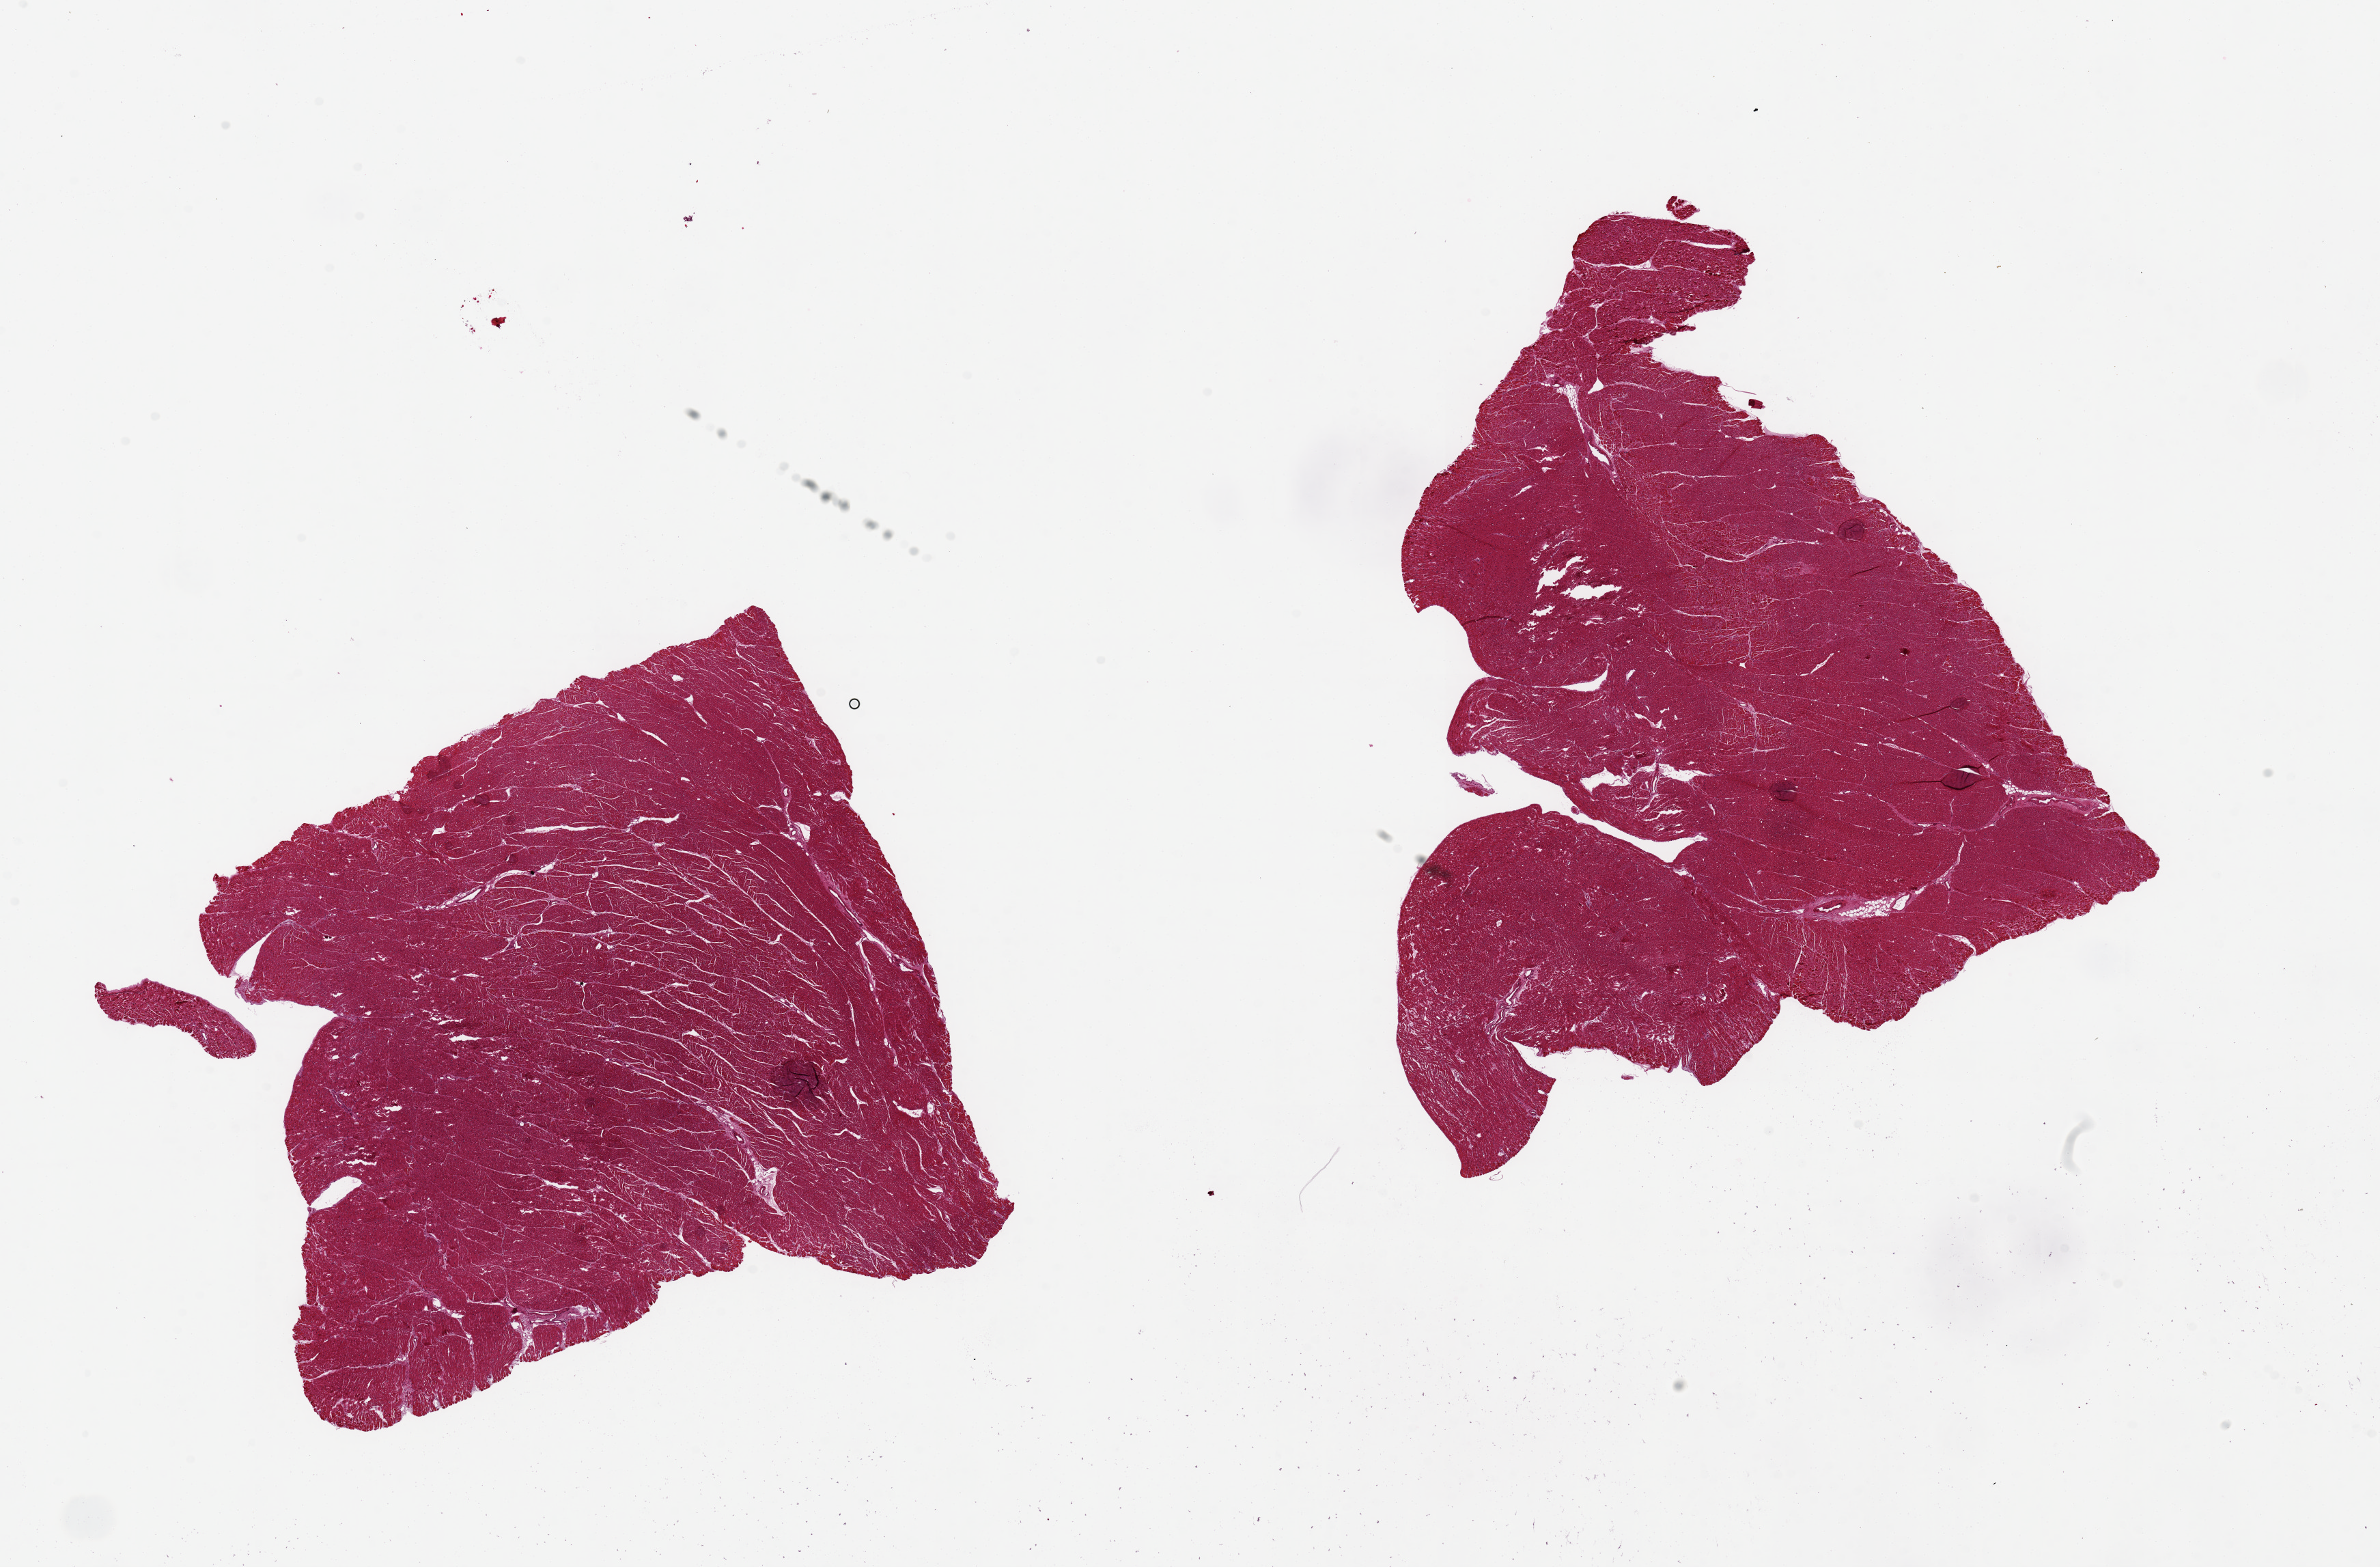
Whole-slide image, hematoxylin and eosin (H&E) stain — whole scanned area (about 27.6 x 18.1 mm, slide scanned at 20x) shown as a low-resolution overview; PAXgene-fixed, paraffin-embedded tissue; section of heart (target tissue); tissue donor sample. Donor sex: male.
* reviewer comment on this tissue sample: 2 pieces, 9x9 & 7x8 mm